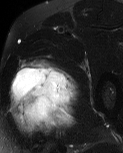
MRI of an extremity soft-tissue mass, one axial slice; position 40 of 60 along the scan axis; T2-weighted fat-saturated; MR volume resampled by the dataset authors to the PET/CT grid (not the native acquisition matrix); 123 × 153 image matrix, field of view 120 × 149 mm. Male patient. Case-level facts recorded for this patient, not image findings: histological type: pleiomorphic liposarcoma; grade: high; site of the primary tumour: left thigh.
Outlined on this slice (expert contour drawn on MRI and transferred to this co-registered scan by the dataset authors):
- gross tumour volume including surrounding oedema: bounding box <9,59,80,137> (left, top, right, bottom; pixels)
- gross tumour volume (mass): <11,68,71,121>